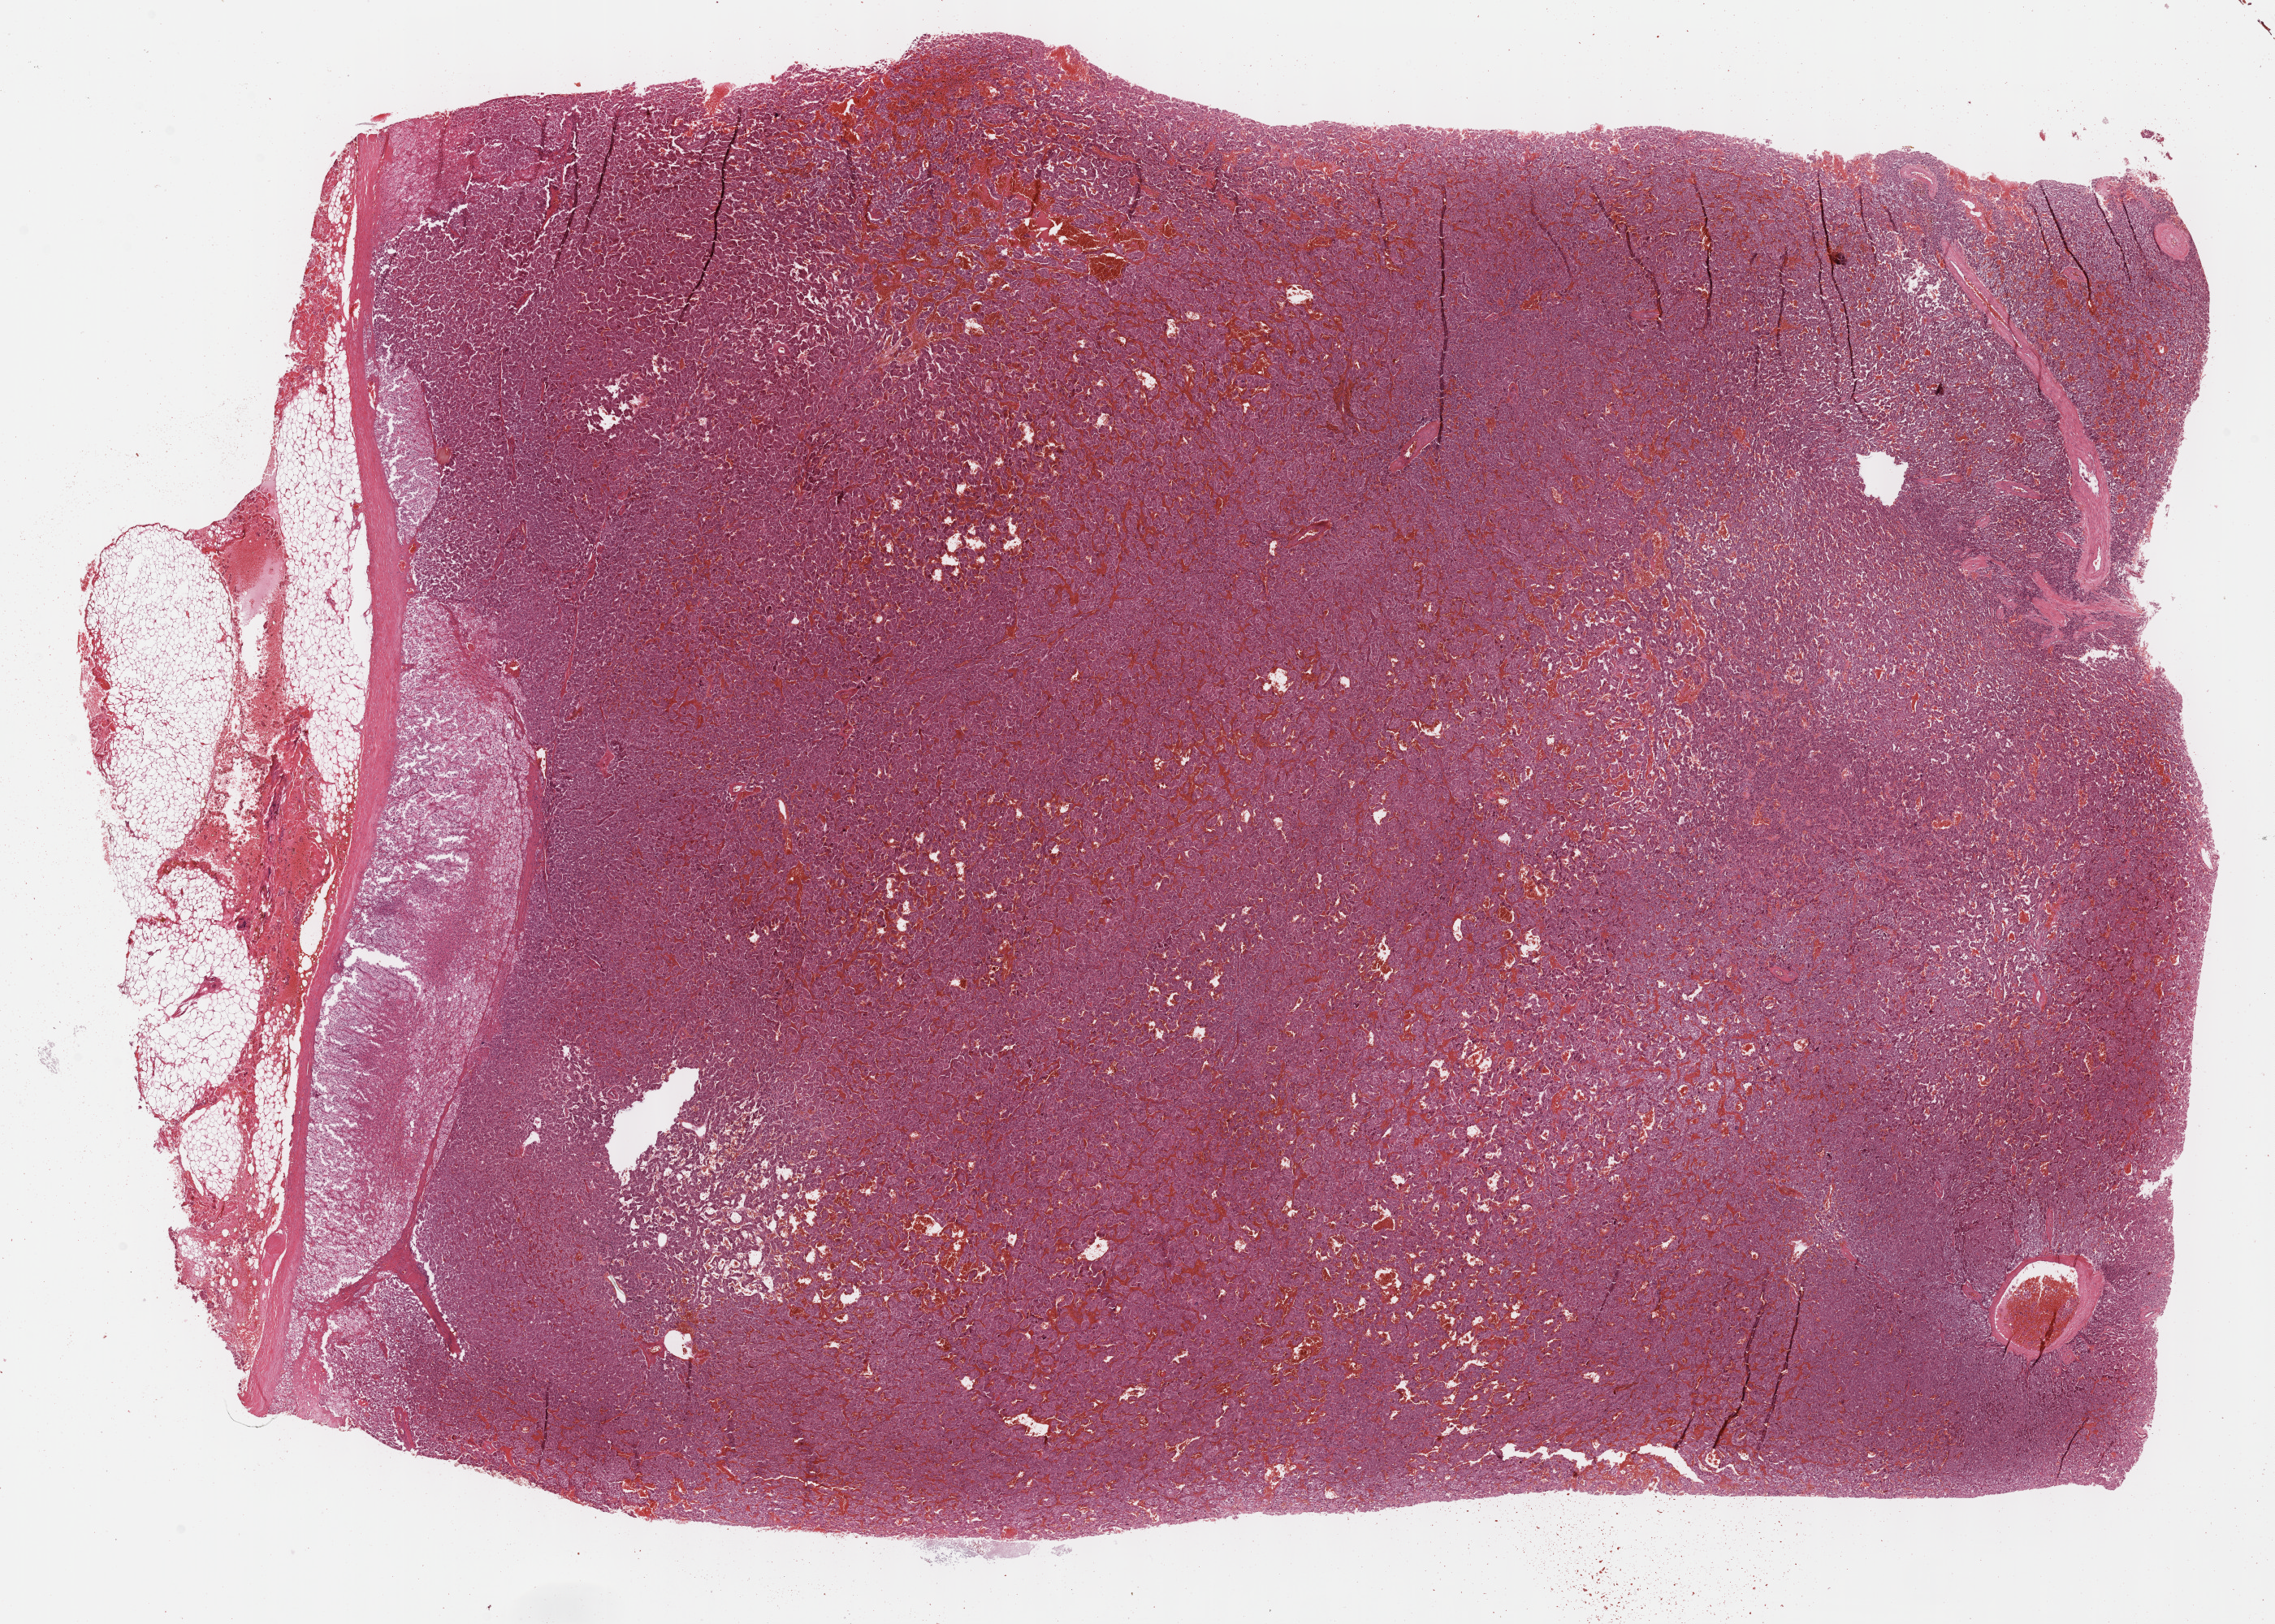
Hematoxylin and eosin (H&E) stained whole-slide image — low-resolution overview of the scanned area, about 22.7 x 16.2 mm. FFPE section. Adrenal gland, primary tumour sample. Patient: male, age at initial diagnosis 52 years.
Laterality: right. Histologic diagnosis: Pheochromocytoma, malignant.